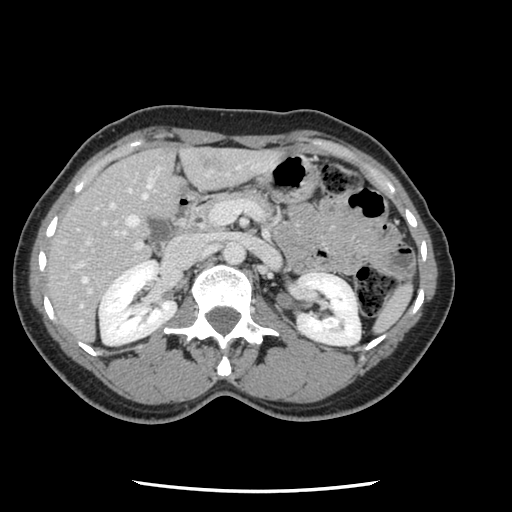
Contrast-enhanced abdominal CT, one axial slice. Position 56 of 134 along the scan axis. 120 kVp. Intravenous contrast given. Soft-tissue window (W 400 / L 40 HU). 512 × 512 image matrix, field of view 330 × 330 mm. Female patient, age 43 years. From the clinical record (not read from this slice): diagnosis: colorectal cancer liver metastases, imaged before liver resection; multiple liver metastases: yes; largest metastasis: 3.4 cm; chemotherapy before resection: no.
Annotated regions visible in this slice (manually delineated by an expert):
- hepatic veins: box from (x=82, y=177) to (x=154, y=283) px
- liver: (x=46, y=147)–(x=281, y=343)
- planned liver remnant (the part of the liver to remain after resection): (x=46, y=147)–(x=180, y=326)
- portal vein (with intrahepatic branches): (x=71, y=166)–(x=267, y=295)
- liver metastasis: (x=204, y=158)–(x=212, y=166)